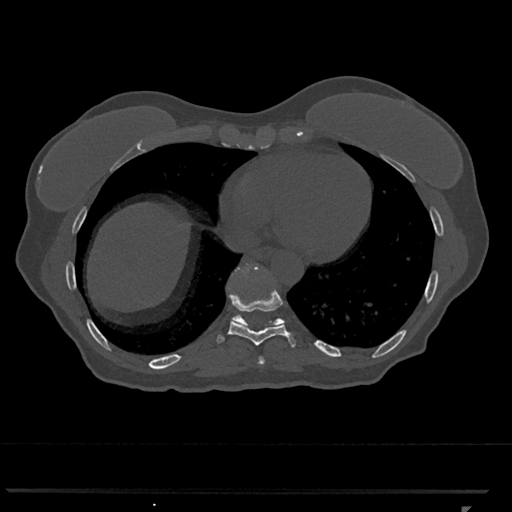
CT including the spine, one axial slice. Position 609 of 793 along the scan axis. Reconstruction kernel Br40s/3. Bone window (W 1800 / L 400 HU). 512 × 512 image matrix, field of view 380 × 380 mm. Female patient, age 62 years. From the clinical record (not read from this slice): primary cancer: renal.
Outlined on this slice (semi-automatically segmented with operator editing):
- T10 vertebra: bounding box [x1, y1, x2, y2] px = [231, 264, 285, 327]
- T8 vertebra: [258, 357, 265, 365]
- T9 vertebra: [217, 289, 296, 347]